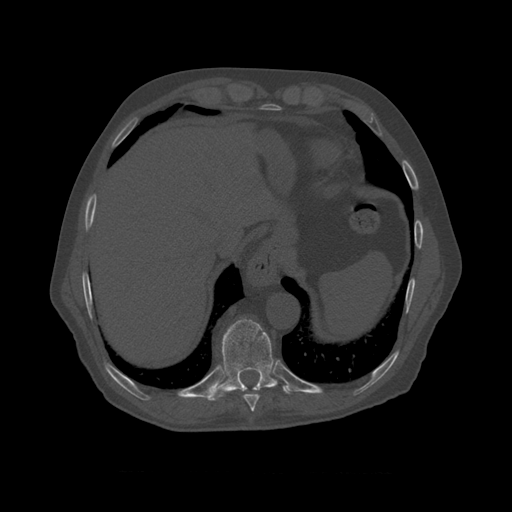
CT including the spine, one axial slice; position 432 of 450 along the scan axis; reconstruction kernel STANDARD; 120 kVp; bone window (W 1800 / L 400 HU); 512 × 512 image matrix, field of view 405 × 405 mm. Patient age 75 years. Case-level facts recorded for this patient, not image findings: primary cancer: prostate.
Structures marked on this image (semi-automatically segmented with operator editing):
- T8 vertebra: bounding box (x1, y1, x2, y2) in pixels: (243, 390, 260, 410)
- T9 vertebra: (216, 318, 288, 398)